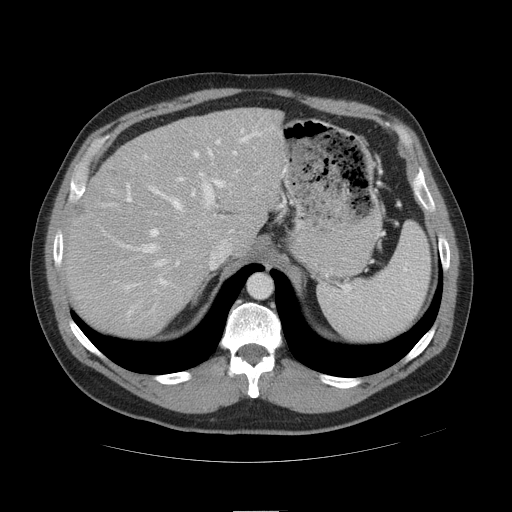
Contrast-enhanced abdominal CT, one axial slice. Position 34 of 49 along the scan axis. Reconstruction kernel STANDARD. Soft-tissue window (W 400 / L 40 HU). 5 mm slice thickness. 512 × 512 image matrix. Male patient, age 52 years. From the clinical record (not read from this slice): diagnosis: colorectal cancer liver metastases, imaged before liver resection; multiple liver metastases: yes; largest metastasis: 5.1 cm.
Structures marked on this image (manually delineated by an expert):
- hepatic veins: box from (x=121, y=147) to (x=237, y=290) px
- liver: (x=66, y=109)–(x=279, y=336)
- planned liver remnant (the part of the liver to remain after resection): (x=135, y=109)–(x=280, y=246)
- portal vein (with intrahepatic branches): (x=102, y=128)–(x=262, y=237)
- liver metastasis: (x=80, y=206)–(x=87, y=216)